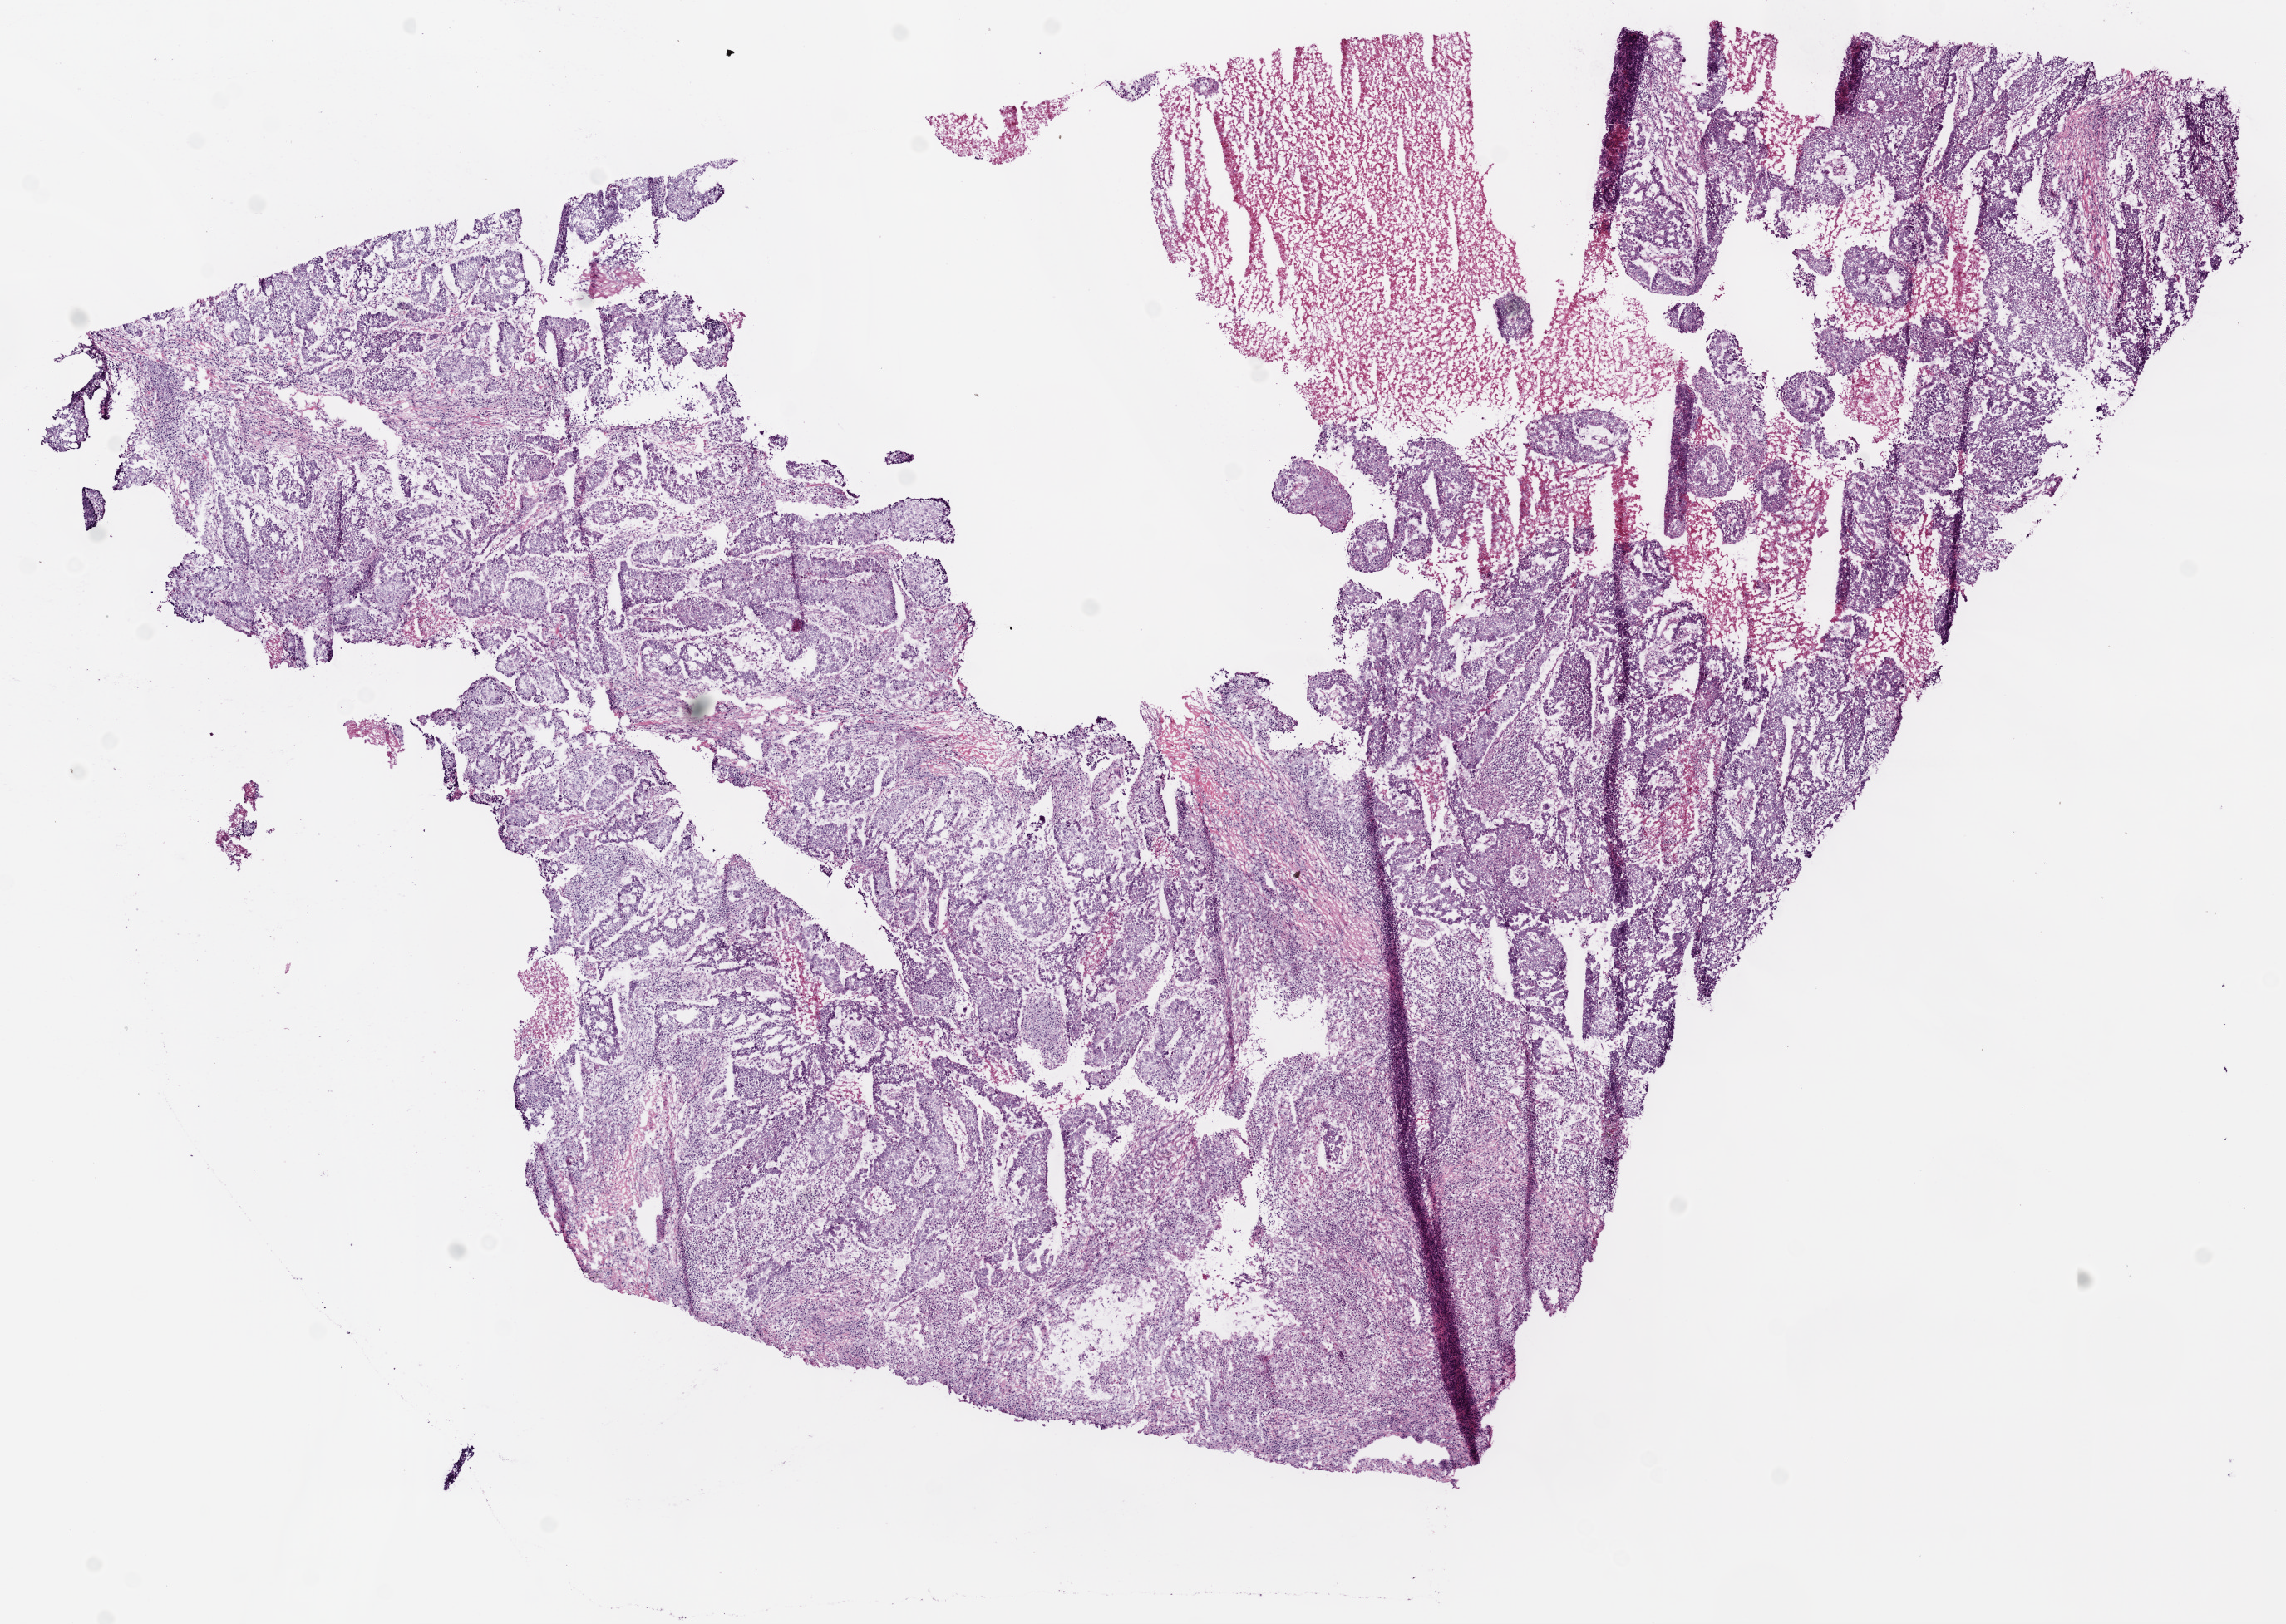
Whole-slide histology image, H&E-stained, low-resolution overview of the scanned area, about 11.0 x 7.8 mm (acquisition: 20x scan), frozen section from the bottom of the tissue portion, lung, primary tumour sample. Female patient; age at initial diagnosis 73 years. Composition of this section per pathologist review: tumour cells 70%, tumour nuclei 65%, normal cells 0%, stromal cells 10%, necrosis 20%.
* AJCC pathologic stage: IB
* diagnosis: Squamous cell carcinoma, NOS (overlapping lesion of lung)